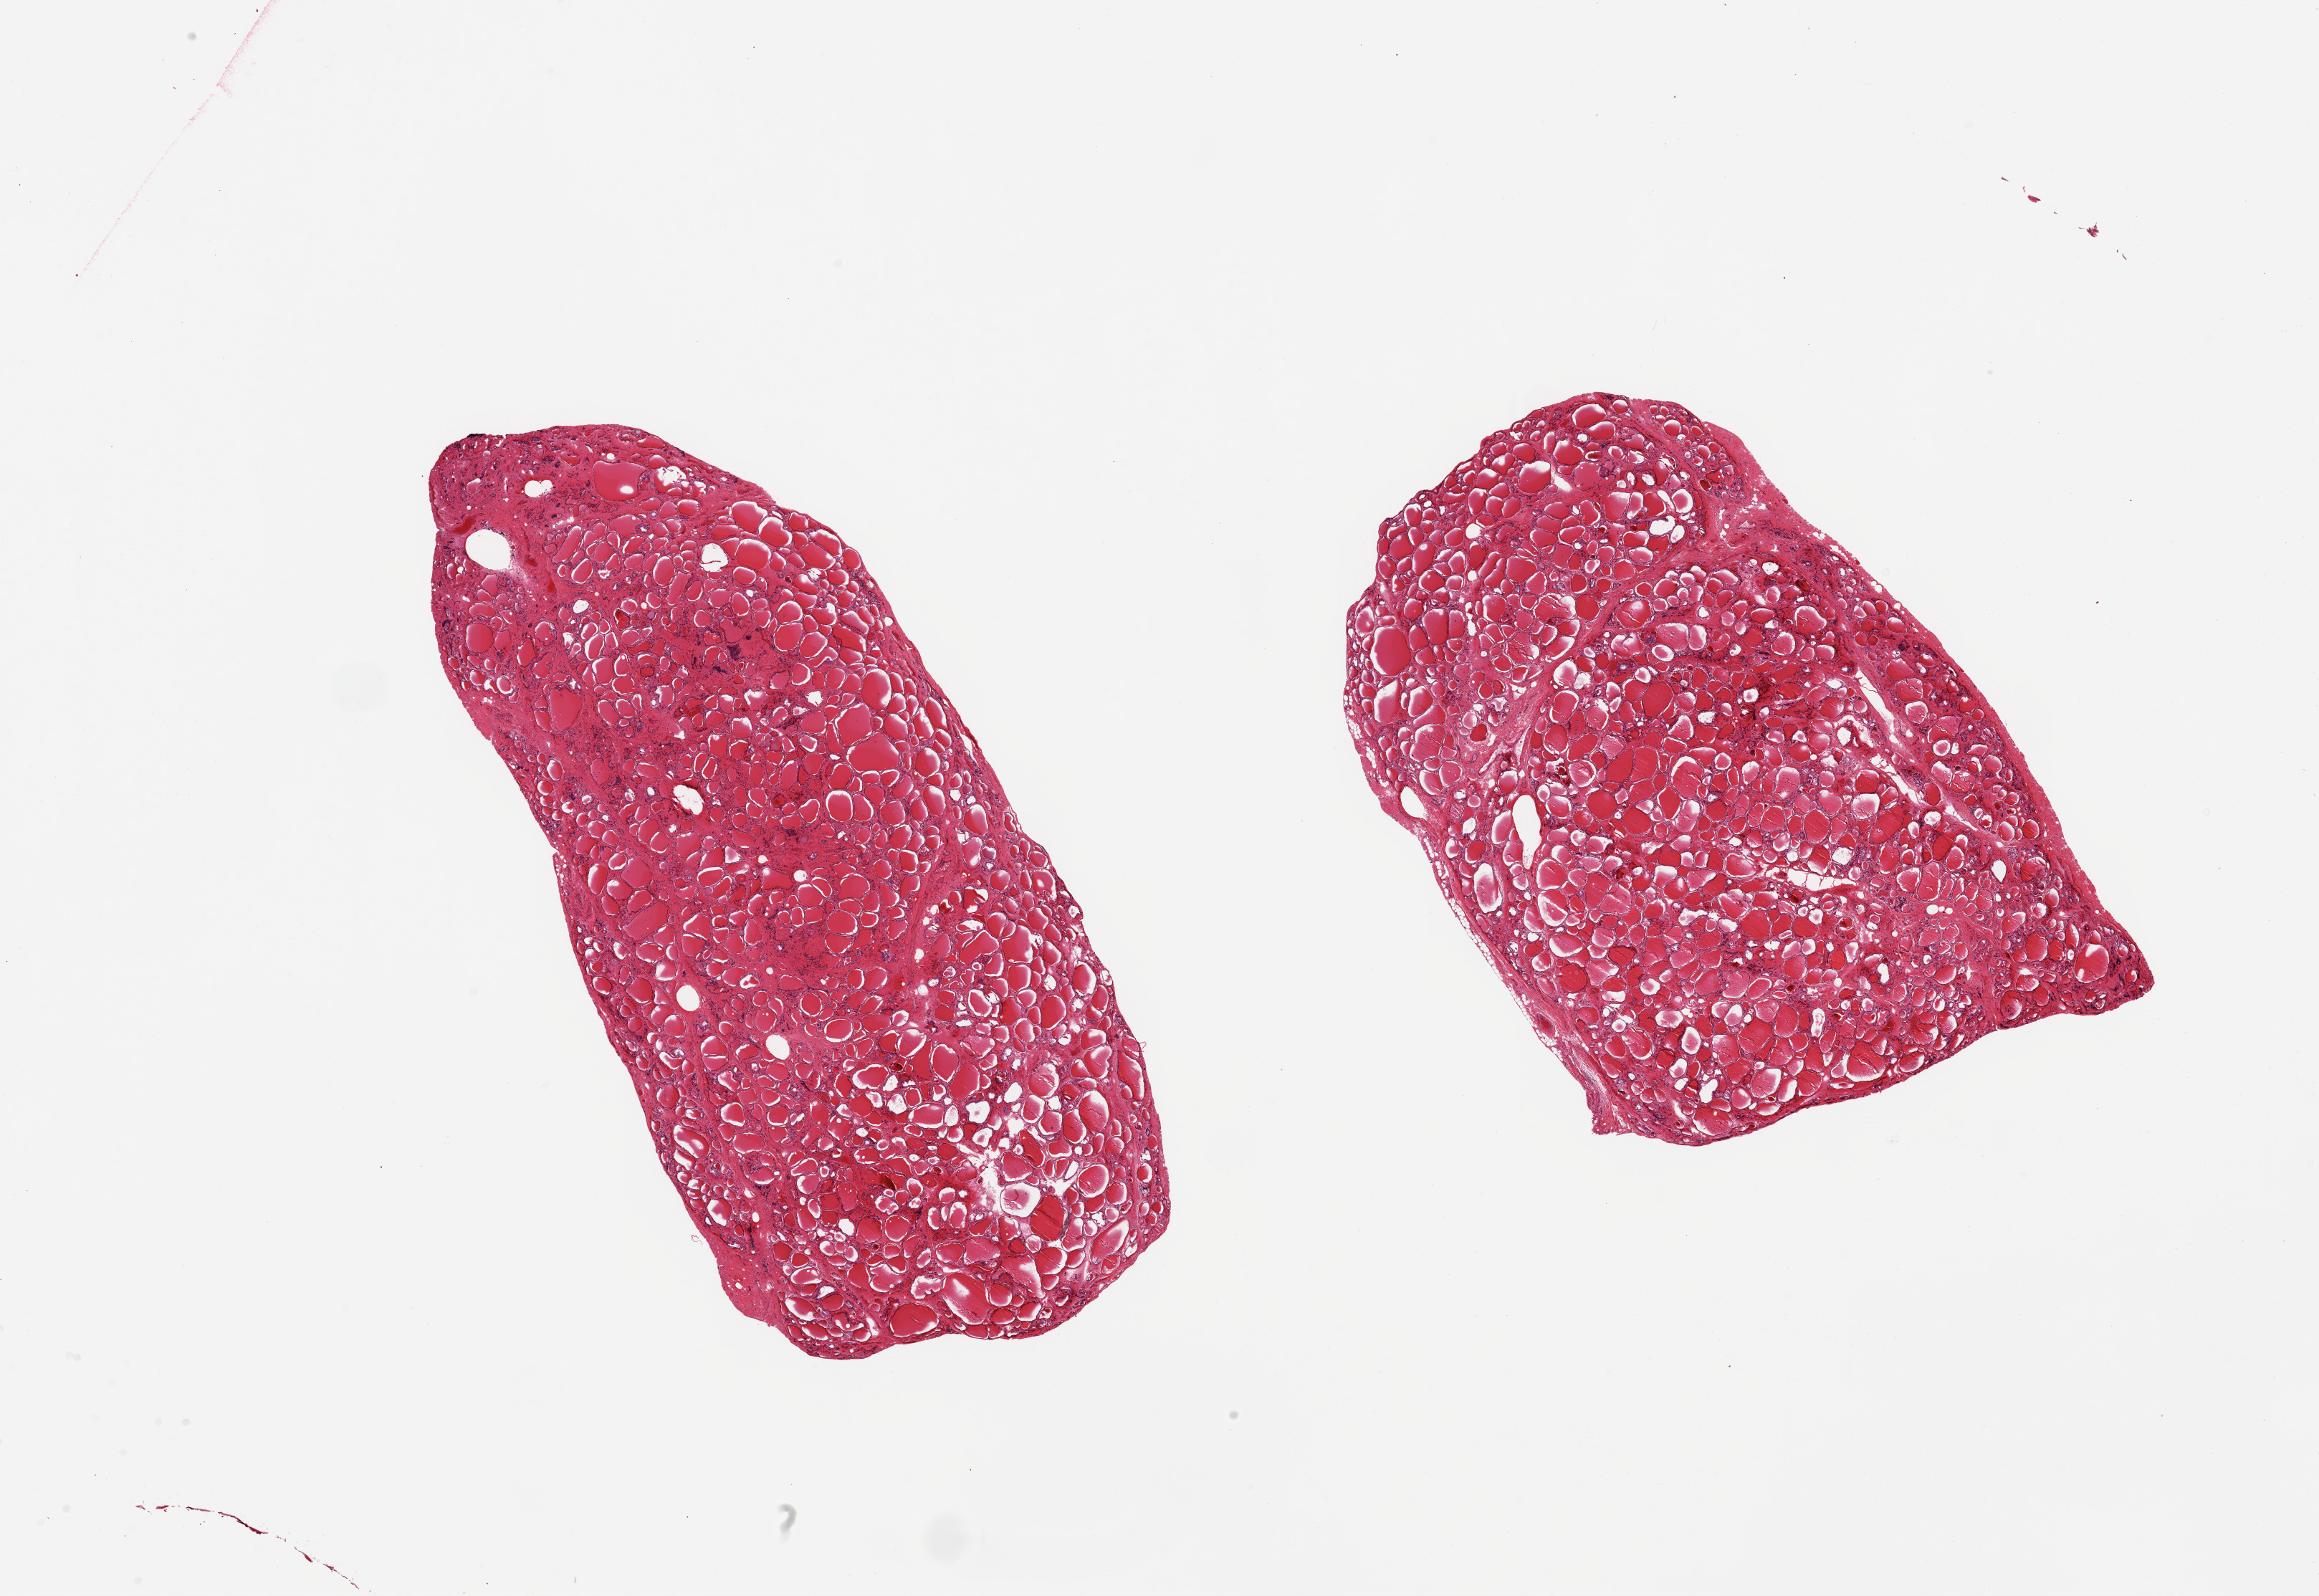
Whole-slide image, H&E stain, a low-resolution overview of the entire scanned area, about 25.6 x 17.6 mm (acquisition: 20x scan). PAXgene-fixed, paraffin-embedded tissue. Sampled site (target tissue): thyroid. Tissue donor sample. Male donor.
Reviewer comment on this tissue sample: 2 pieces; interstitial fibrosis and scattered collapsed follicles; congestion.